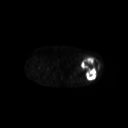
FDG PET of an extremity soft-tissue mass (from a PET/CT study), one axial slice. Slice 228 of 267 in the series (ordered by position). 3.27 mm slice thickness. 128 × 128 image matrix, field of view 700 × 700 mm. Female patient, age 62 years. Case-level facts recorded for this patient, not image findings: histological type: undifferentiated – high grade; grade: high; site of the primary tumour: left thigh.
Structures marked on this image (expert contour drawn on MRI and transferred to this co-registered scan by the dataset authors):
- gross tumour volume including surrounding oedema: bounding box <81,56,100,80> (left, top, right, bottom; pixels)
- gross tumour volume (mass): <81,56,99,80>